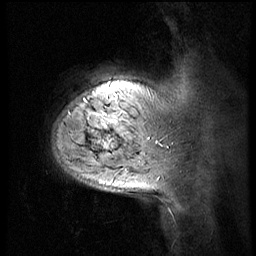
Breast MRI (dynamic contrast-enhanced), one sagittal slice; slice 8 of 56 in the series (ordered by position); 4 images stored at this slice position (order not interpretable as contrast timing); 1.5 T; TE 4.2 ms, TR 8.9 ms; 2.5 mm slice thickness; 256 × 256 image matrix, field of view 220 × 220 mm. Patient: female, 51 years. Case-level facts recorded for this patient, not image findings: setting: breast cancer imaged before/during neoadjuvant chemotherapy; receptor status: triple-negative.
Outlined on this slice (semi-automatically segmented with operator editing):
- analysis volume of interest (the breast-tissue region the enhancement analysis was run in; not a lesion): bounding box [x1, y1, x2, y2] px = [50, 70, 150, 173]
- tumour enhancement mask (voxels above the 140 % enhancement threshold inside the analysis volume of interest): [101, 140, 113, 149]